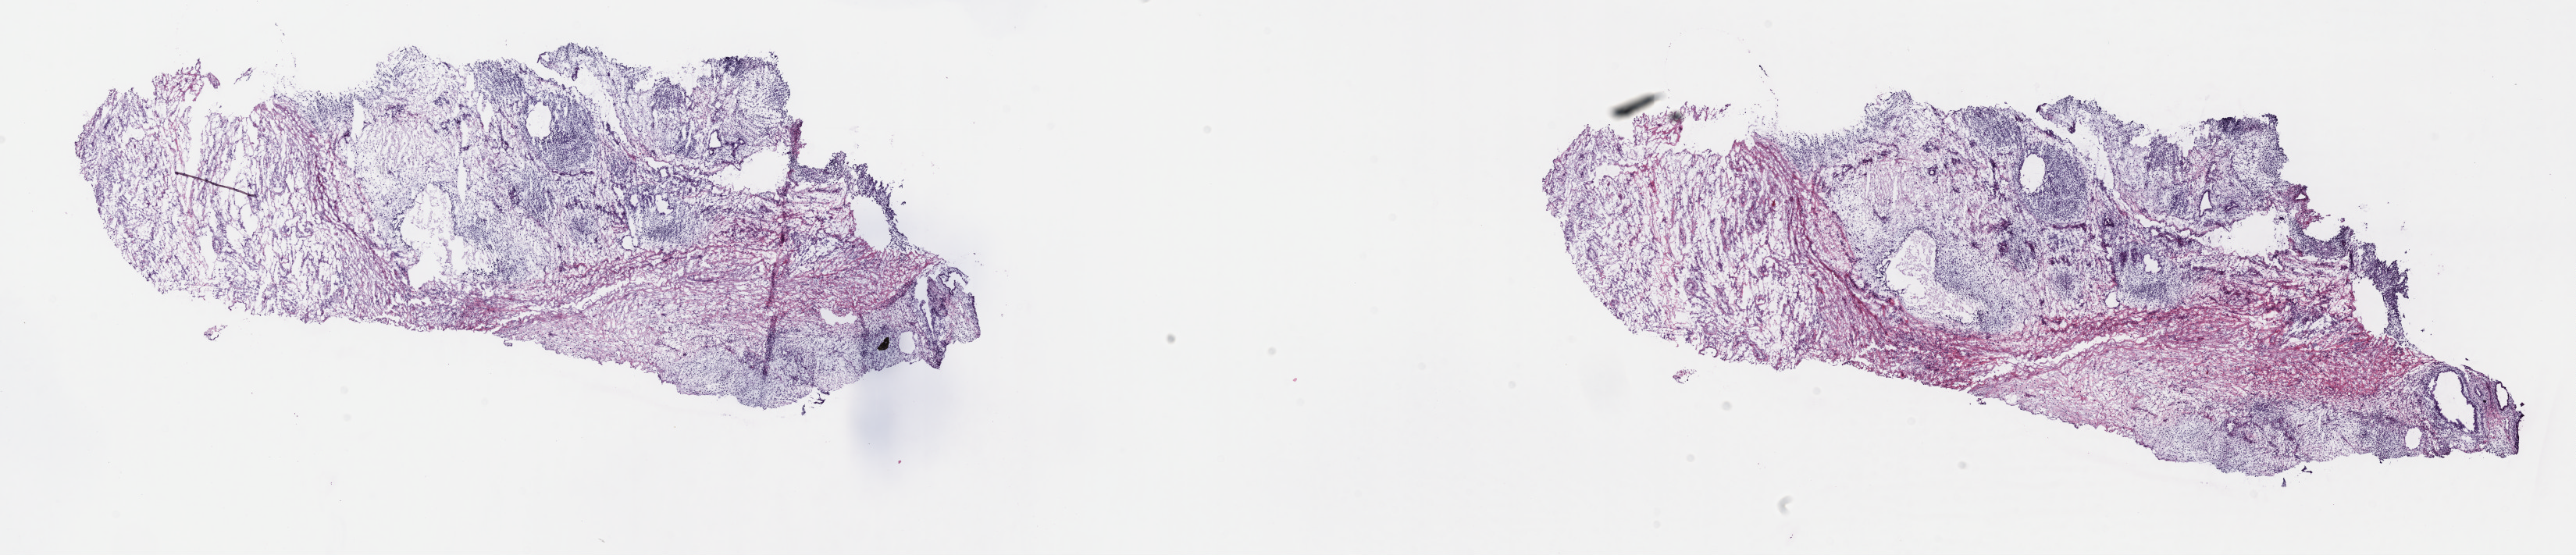
Digitized H&E tissue section (whole slide) — low-resolution overview of the scanned area, about 26.7 x 5.7 mm (acquisition: 40x scan). Frozen section from the top of the tissue portion. Sample: primary tumour, testis. Male, age 28 years at initial diagnosis. Pathologist review of this section (percent, as recorded): tumour cells 100%, tumour nuclei 80%, normal cells 0%, stromal cells 0%, necrosis 0%. Infiltration values recorded for this section: lymphocyte infiltration 1%, monocyte infiltration 0%, neutrophil infiltration 0%.
AJCC pathologic stage: IS (5th edition). Diagnosis: Teratoma, benign.